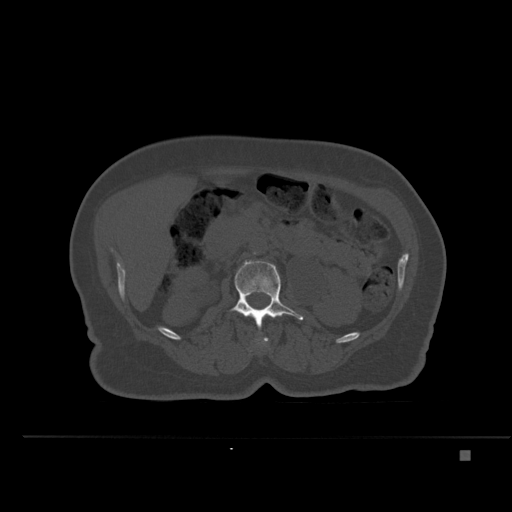
CT including the spine, one axial slice. Slice 217 of 477 in the series (ordered by position). Bone window (W 1800 / L 400 HU). 1.5 mm slice thickness. 512 × 512 image matrix, field of view 422 × 422 mm. Female patient, age 74 years. From the clinical record (not read from this slice): primary cancer: colon.
Outlined on this slice (semi-automatically segmented with operator editing):
- L1 vertebra: bounding box <256,315,272,347> (left, top, right, bottom; pixels)
- L2 vertebra: <229,261,304,328>